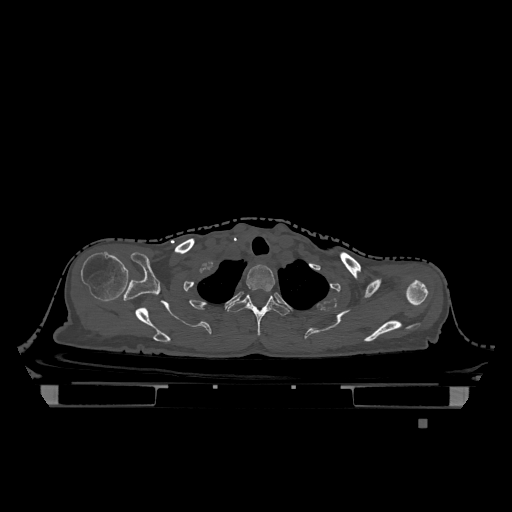
CT including the spine, one axial slice. Position 976 of 1317 along the scan axis. Bone window (W 1800 / L 400 HU). 512 × 512 image matrix, field of view 500 × 500 mm. Female patient, age 74 years. From the clinical record (not read from this slice): primary cancer: lung; vertebrae with lytic lesions (as recorded): T1, T4, T5, T6, L4, L5.
Annotated regions visible in this slice (semi-automatically segmented with operator editing):
- T1 vertebra: box from (x=246, y=265) to (x=275, y=292) px
- T2 vertebra: (x=228, y=295)–(x=289, y=336)